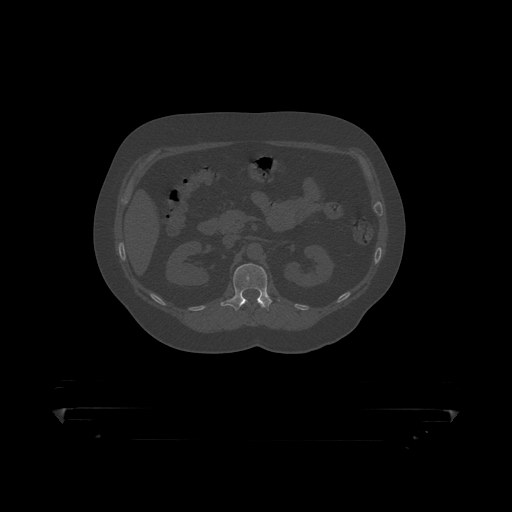
CT including the spine, one axial slice. Slice 151 of 390 in the series (ordered by position). Reconstruction kernel STANDARD. Bone window (W 1800 / L 400 HU). 1.25 mm slice thickness. 512 × 512 image matrix, field of view 650 × 650 mm. Patient: male, 60 years. Case-level facts recorded for this patient, not image findings: primary cancer: prostate.
Structures marked on this image (semi-automatically segmented with operator editing):
- L1 vertebra: box from (x=221, y=264) to (x=280, y=312) px
- T12 vertebra: (x=242, y=301)–(x=269, y=311)